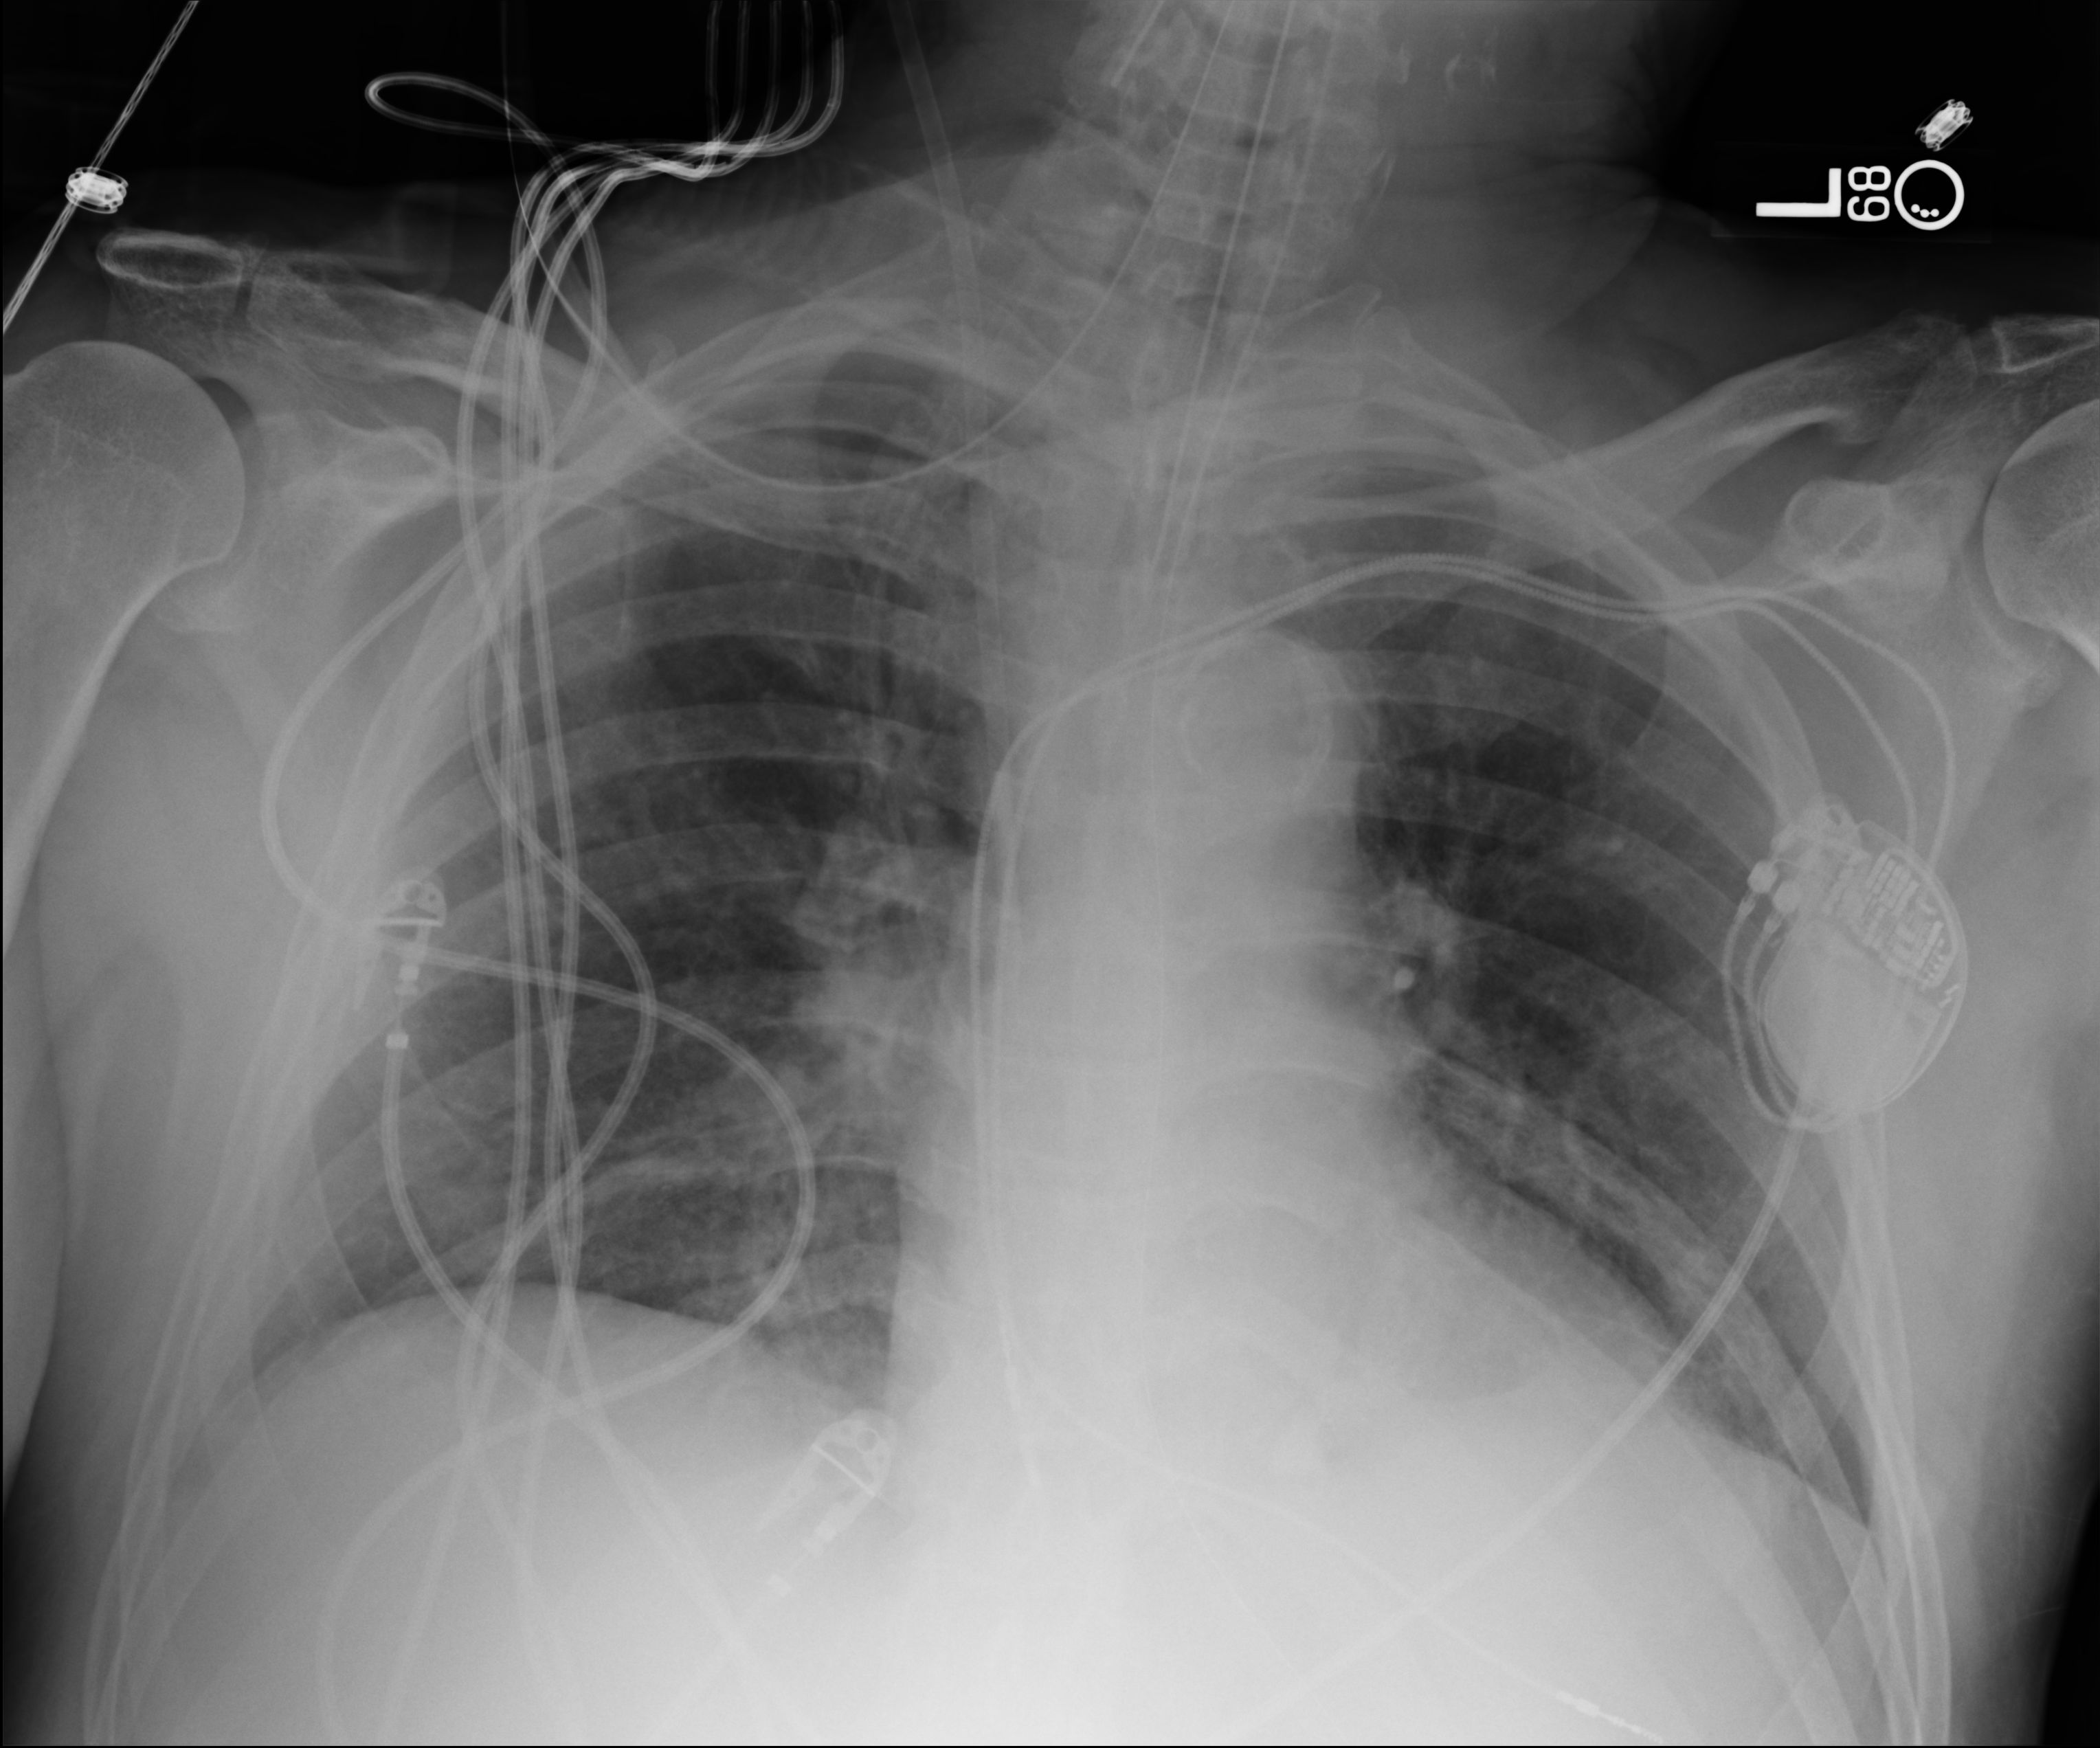
Bedside chest radiograph (computed radiography). Patient hospitalised with COVID-19; male, aged 60–74 years.
Hospital-stay facts (about this admission, not read from this image; timing relative to this image not recorded):
- mechanically ventilated during this hospital stay: yes